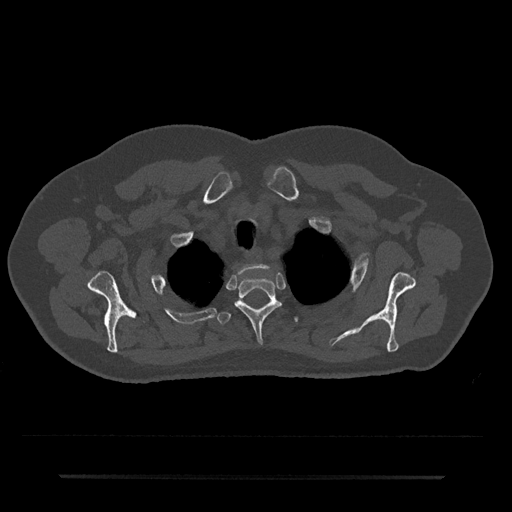
CT including the spine, one axial slice; position 601 of 797 along the scan axis; reconstruction kernel Br40s/3; bone window (W 1800 / L 400 HU); 0.5 mm slice thickness; 512 × 512 image matrix, field of view 437 × 437 mm. Male patient, age 69 years. Case-level facts recorded for this patient, not image findings: primary cancer: prostate.
Annotated regions visible in this slice (semi-automatically segmented with operator editing):
- T1 vertebra: bounding box (x1, y1, x2, y2) in pixels: (238, 264, 268, 275)
- T2 vertebra: (234, 278, 281, 343)
- T3 vertebra: (217, 301, 298, 325)